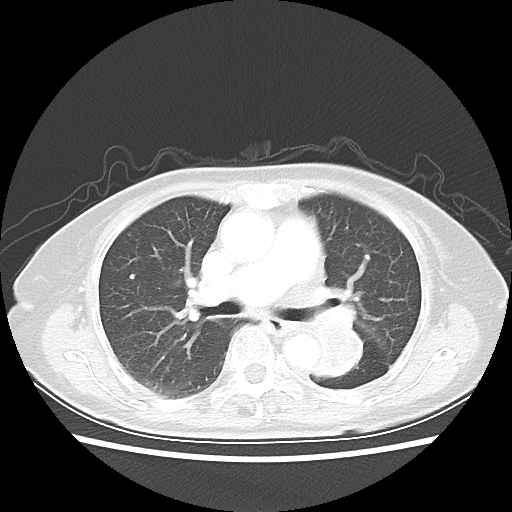
Chest CT, one axial slice. Slice 30 of 50 in the series (ordered by position). Reconstruction kernel LUNG. 80 kVp. Lung window (W 1500 / L -600 HU). 5 mm slice thickness. 512 × 512 image matrix. Patient: female, 81 years. Case-level facts recorded for this patient, not image findings: clinical TNM (as recorded): T2 N0 M1a.
Structures marked on this image (rectangle marked by the reading radiologist):
- lung tumour (recorded histology: squamous cell carcinoma): bounding box (x1, y1, x2, y2) in pixels: (310, 321, 369, 392)